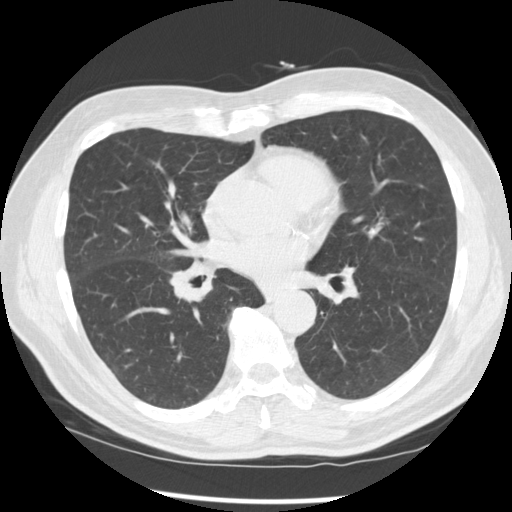
Axial slice from a low-dose chest CT screening exam, first (baseline) screen, lung window (W 1500 / L -600 HU), 2.5 mm slice thickness, slice 139 of 277 in the series, 512 × 512 image matrix, field of view 365 × 365 mm. Male, age 67 years at enrolment.
- Expert reader's lesion annotation, box from (x=155, y=245) to (x=227, y=313) px.
- Screening reader's record for this exam (one nodule recorded; not confirmed to be the boxed lesion): non-calcified nodule or mass ≥4 mm, left lower lobe, 15 × 15 mm, spiculated (stellate) margins, soft tissue attenuation.
- Note: the box lies in the patient's right hemithorax on this image, whereas the reader's record names the left lung; they may be different findings.
- Later outcome: lung cancer diagnosed 49 days after this screen — squamous cell carcinoma, NOS, right middle lobe, poorly differentiated (G3), stage IIB (AJCC 6th edition), 35 mm at pathology.